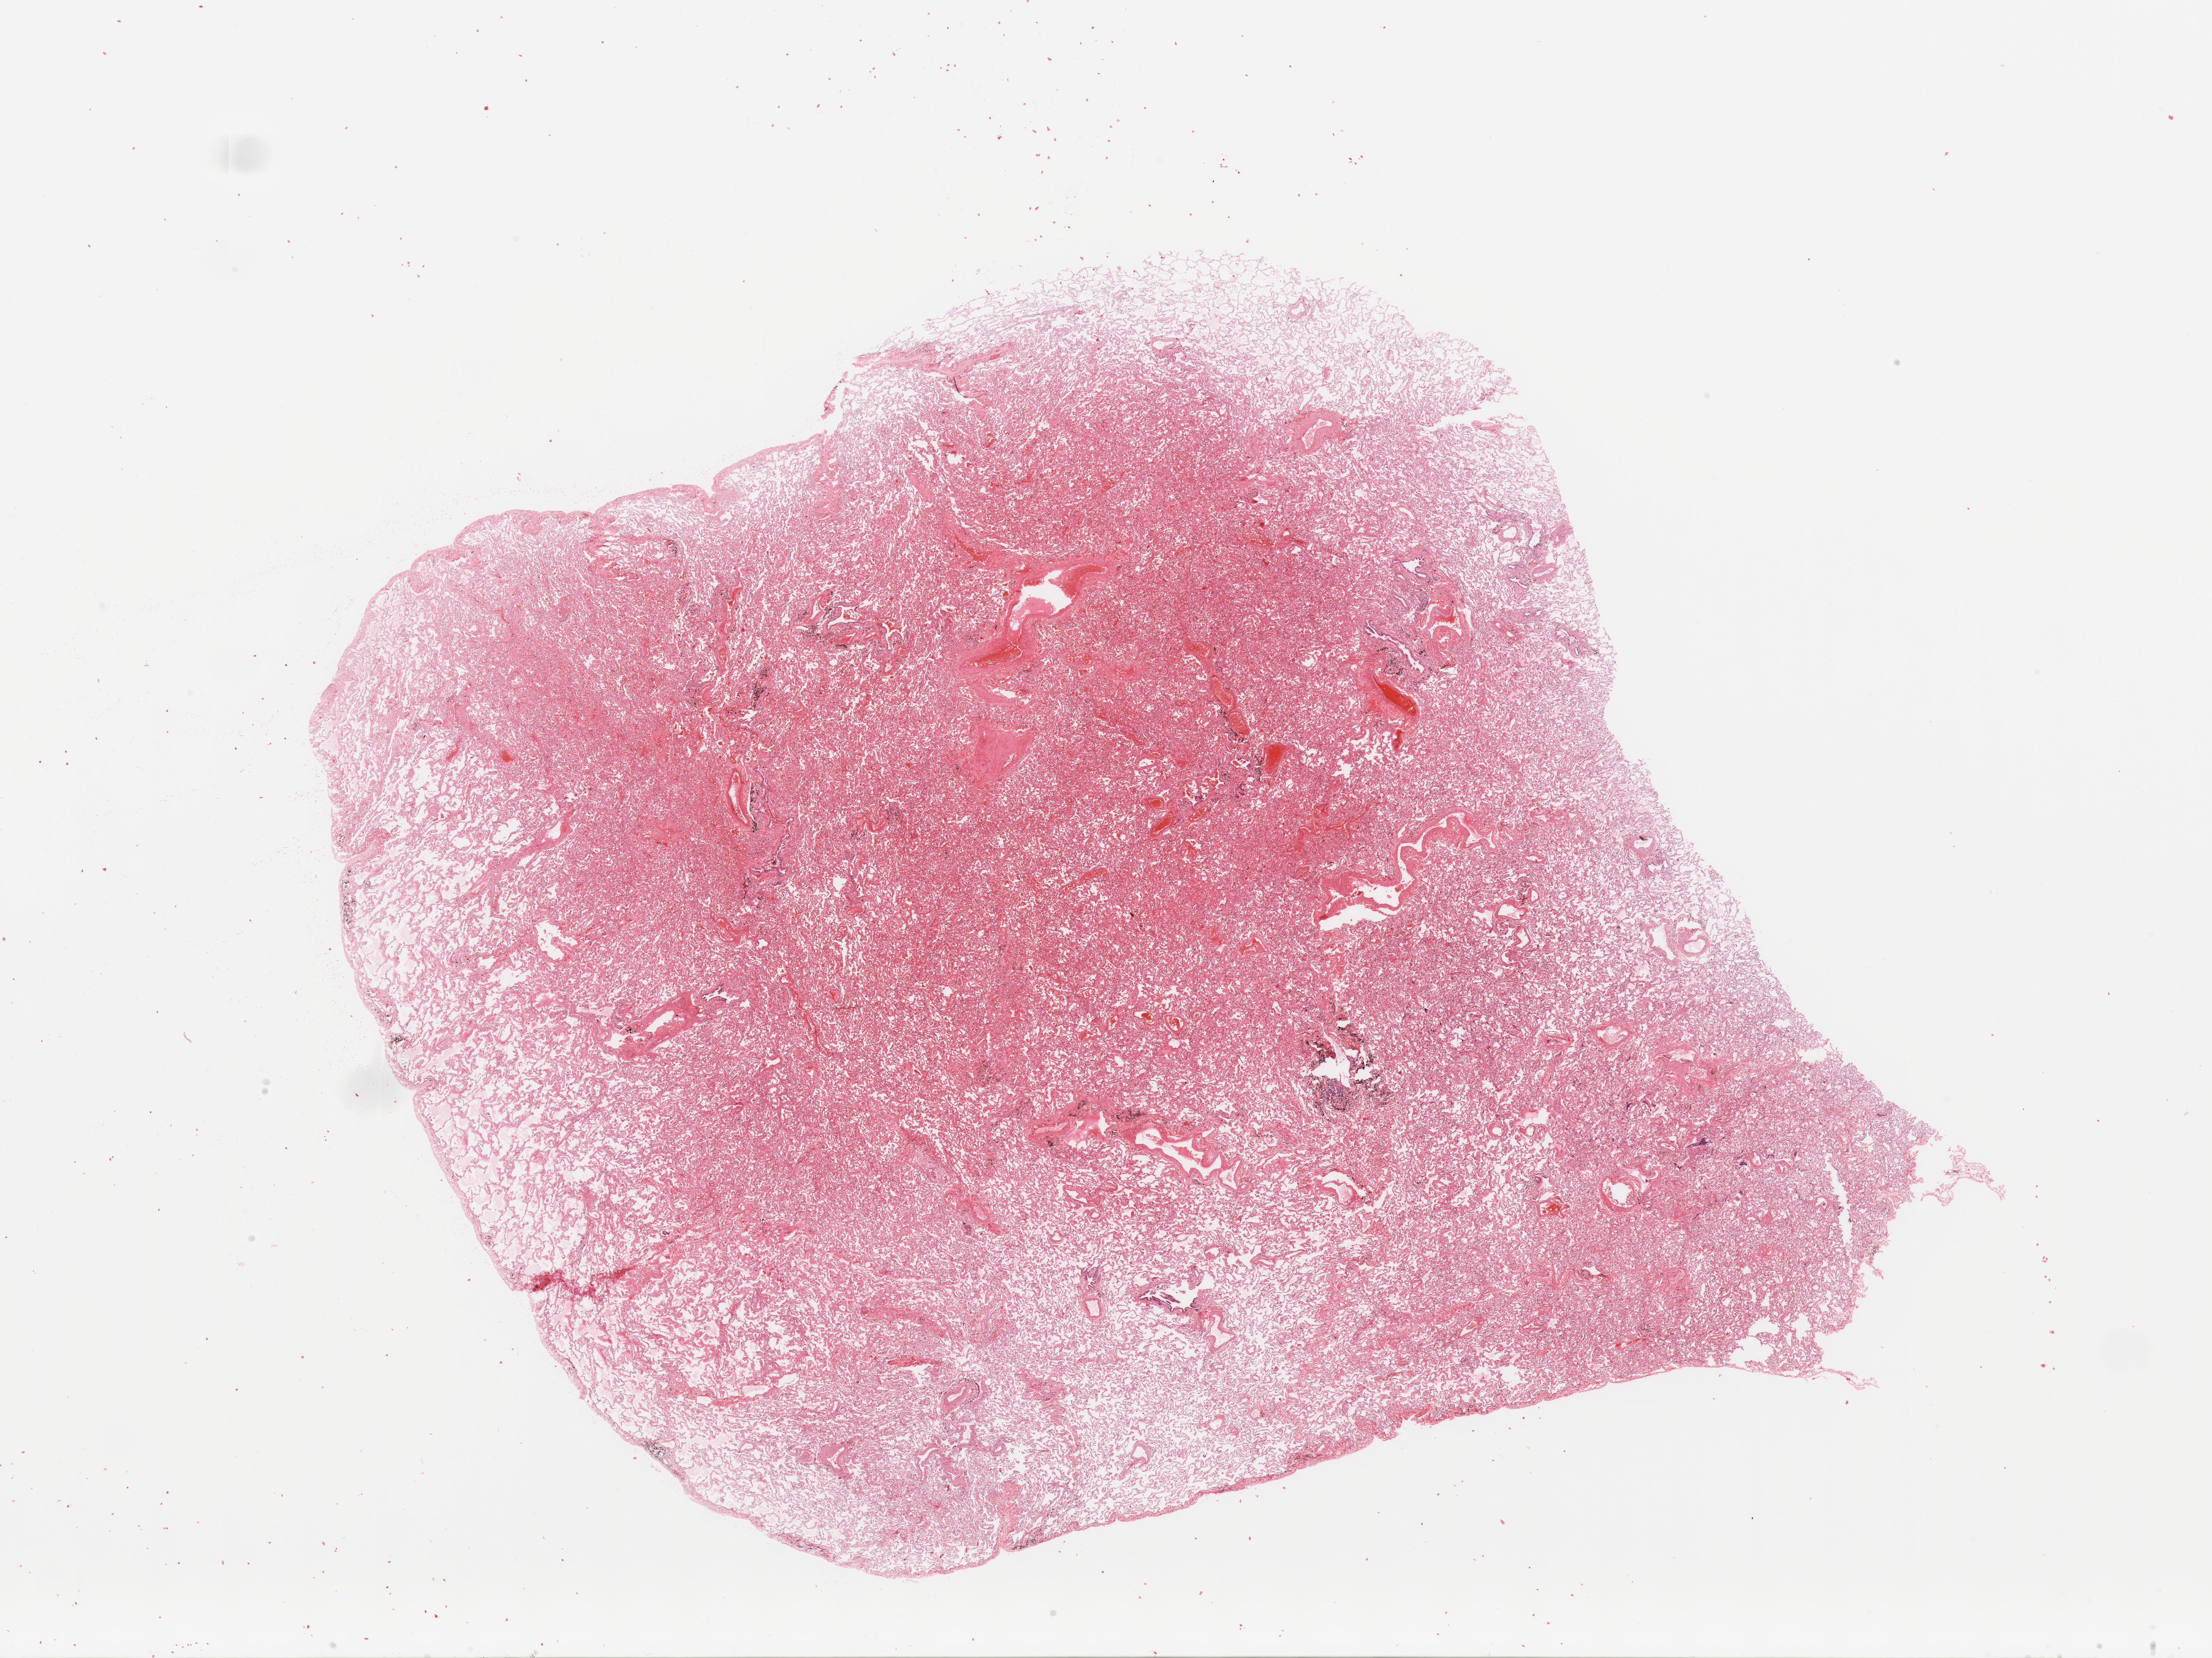
Whole-slide histology image, H&E, a low-resolution overview of the entire scanned area, about 28.5 x 21.4 mm (acquisition: 20x scan); normal (non-tumour) tissue sample, sampled site: lung. Female, 54 y/o.
This section: normal (non-tumour) tissue from the same patient. Patient diagnosis: Adenocarcinoma, NOS.